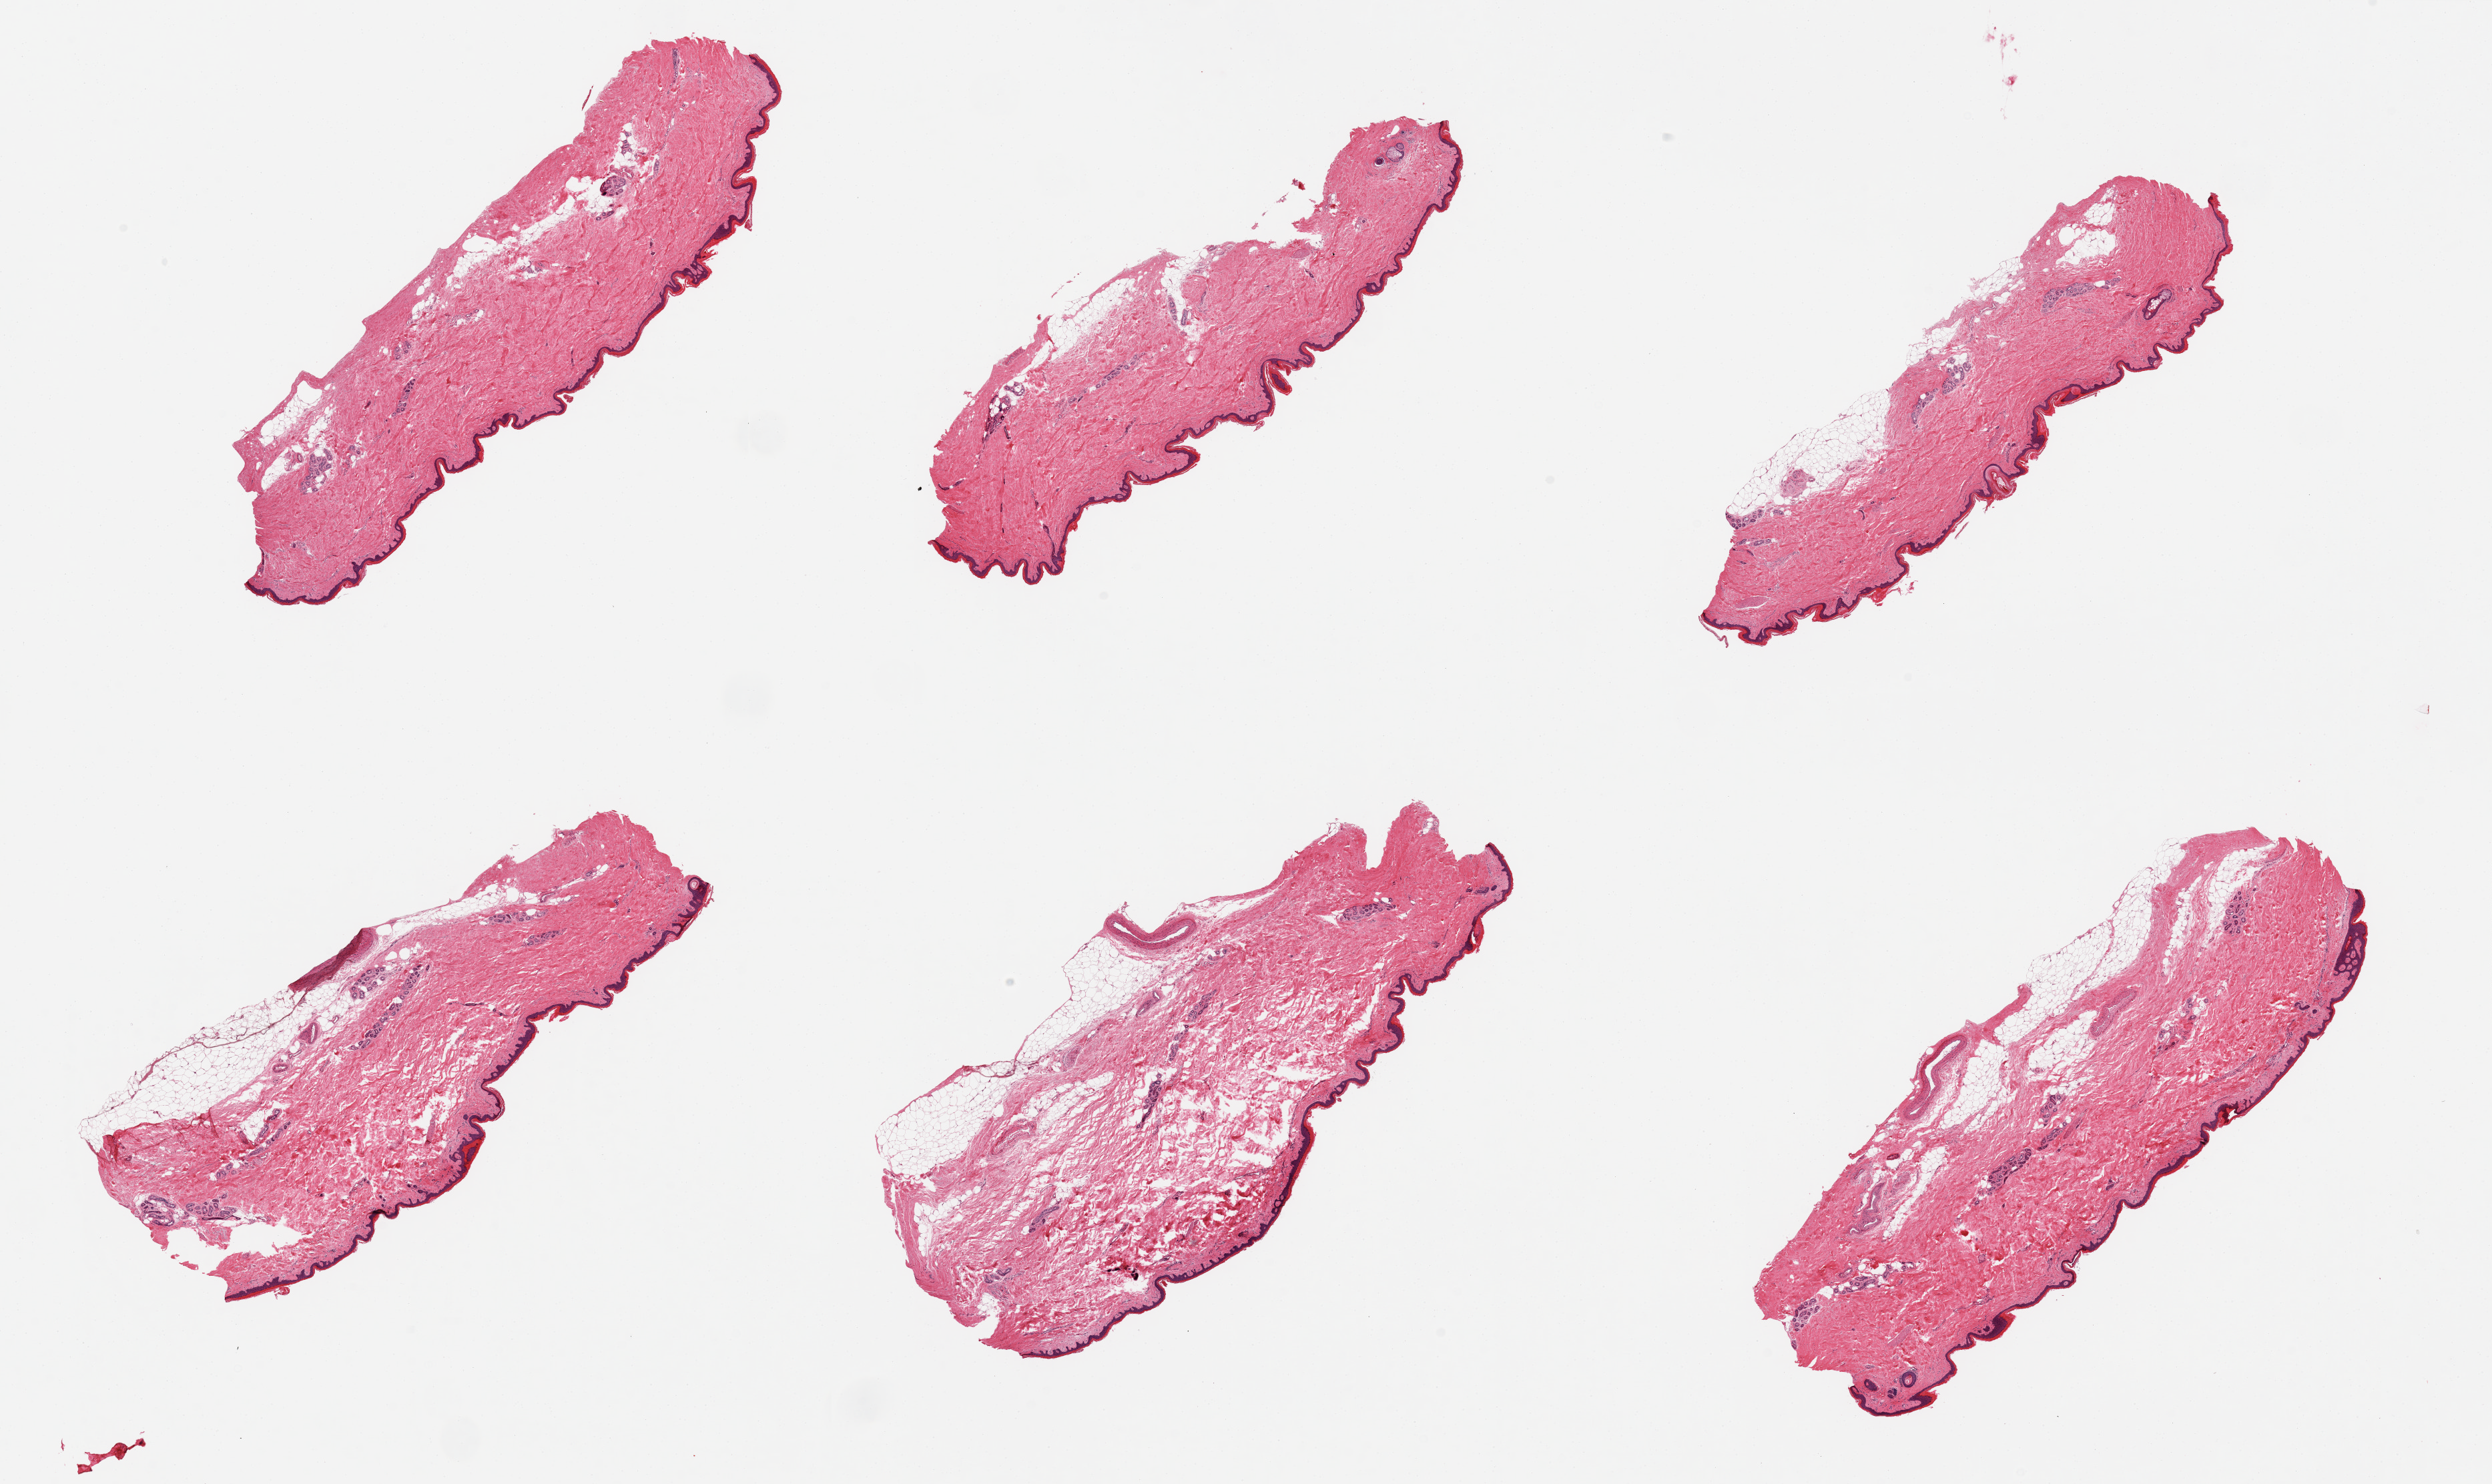
Digitized H&E-stained section — whole scanned area (about 29.5 x 17.6 mm, from a 20x scan) shown as a low-resolution overview, PAXgene-fixed paraffin-embedded (PFPE) section, sampled site (target tissue): skin of lower leg, donor tissue sample.
* review note (as recorded): 6 pieces focal adherent fat, minimal; Squamous epithelium is ~50 microns